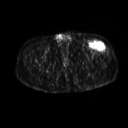
FDG PET of an extremity soft-tissue mass (from a PET/CT study), one axial slice; 3.27 mm slice thickness; 128 × 128 image matrix, field of view 500 × 500 mm. Patient: male, 64 years. From the clinical record (not read from this slice): histological type: extraskeletal osteosarcoma; grade: high; site of the primary tumour: thigh.
Structures marked on this image (expert contour drawn on MRI and transferred to this co-registered scan by the dataset authors):
- gross tumour volume (mass): bounding box [x1, y1, x2, y2] px = [90, 42, 105, 50]